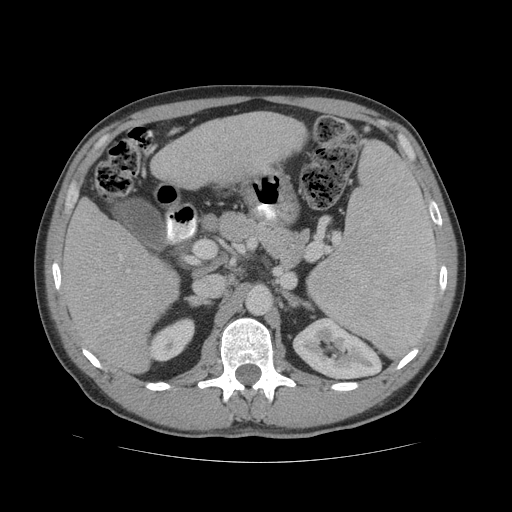
Contrast-enhanced abdominal CT (liver protocol), one axial slice. Slice 30 of 81 in the series (ordered by position). 140 kVp. Soft-tissue window (W 400 / L 40 HU). 2.5 mm slice thickness. 512 × 512 image matrix. From the clinical record (not read from this slice): diagnosis: hepatocellular carcinoma (patient treated with transarterial chemoembolisation; whether this scan precedes or follows treatment is not stated here); TNM stage (as recorded): Stage-IVB; Child-Pugh class: B; tumour differentiation: well differentiated; tumour nodularity: multinodular.
Annotated regions visible in this slice (semi-automatic segmentation, software-assisted and operator-edited):
- liver parenchyma outside the tumour (the mass and vessels are separate outlines, so this box may not span the whole liver): bounding box <62,112,306,372> (left, top, right, bottom; pixels)
- liver vessels: <118,255,121,315>